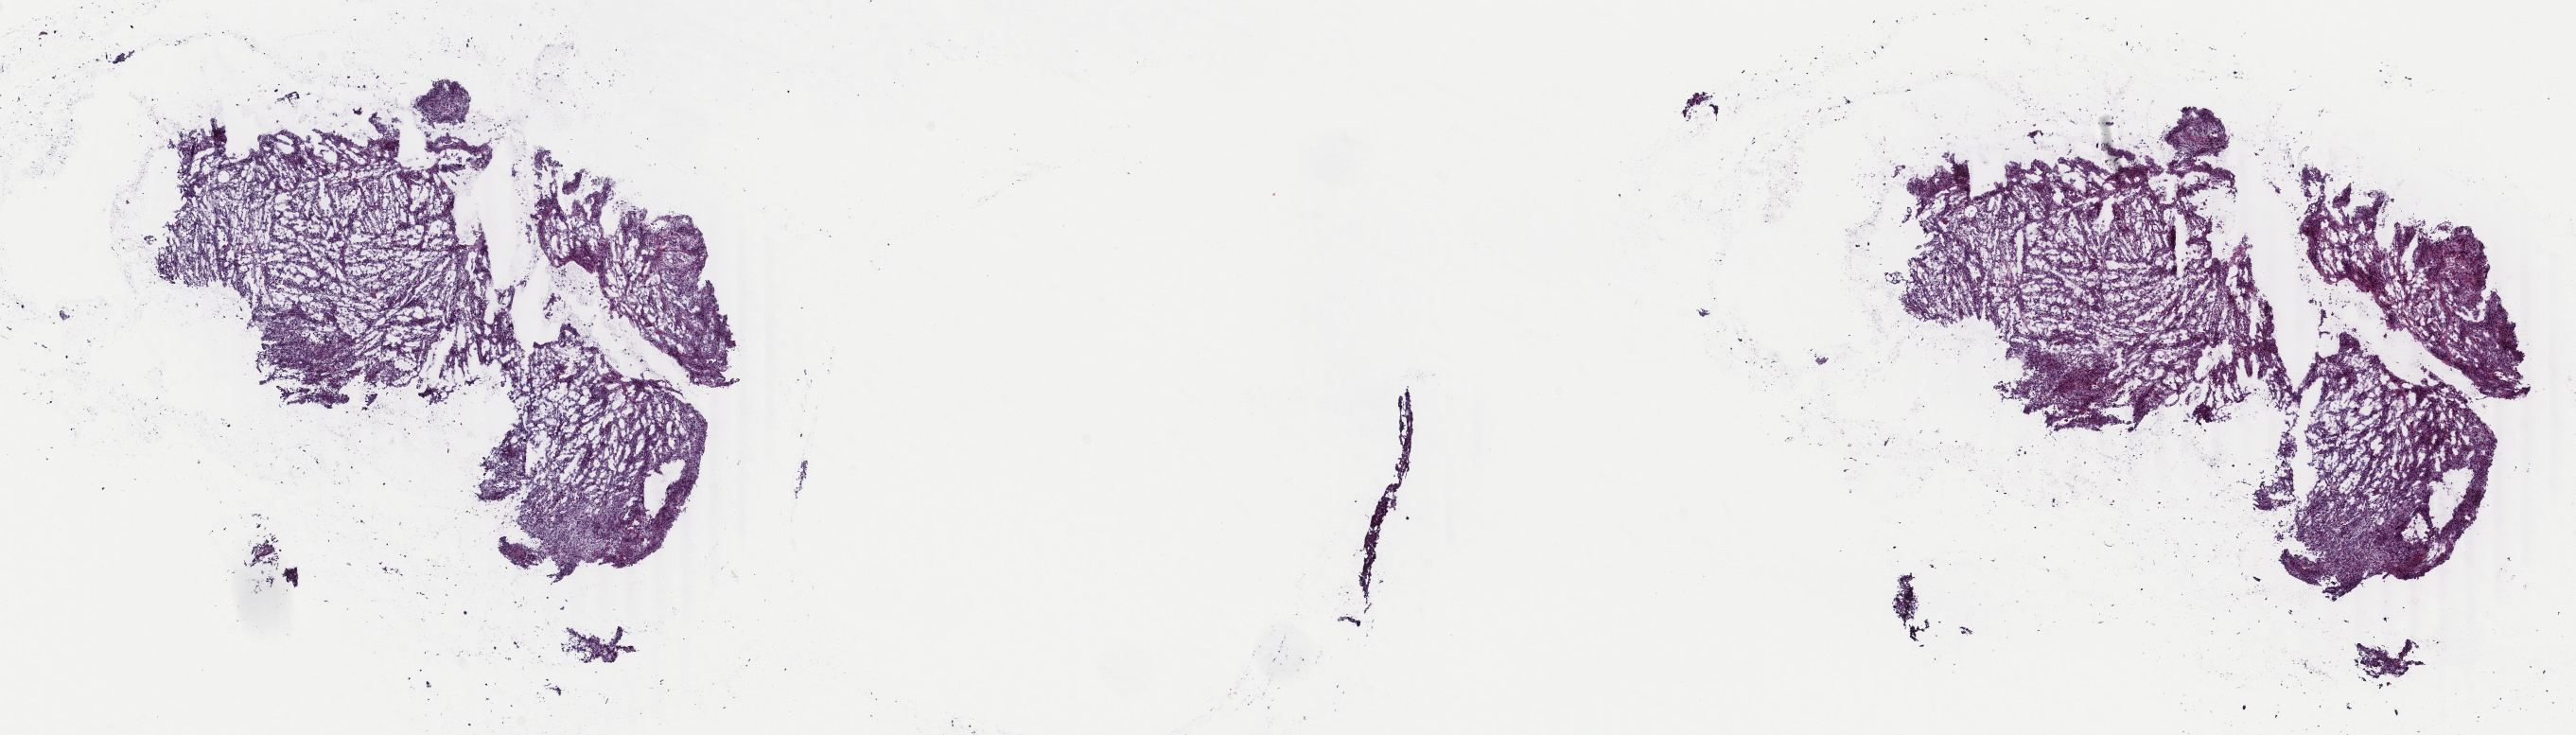
Whole-slide histology image, H&E-stained, whole scanned area (about 21.7 x 6.2 mm) shown as a low-resolution overview; frozen section from the top of the tissue portion; sample: primary tumour, uterus. Patient: female, age at initial diagnosis 61 years. Pathologist review of this section (percent, as recorded): tumour cells 60%, tumour nuclei 60%, normal cells 10%, stromal cells 15%, necrosis 15%. Inflammatory infiltration, as recorded: lymphocyte infiltration 70%, monocyte infiltration 15%, neutrophil infiltration 5%.
Pathologic diagnosis: Mullerian mixed tumor. Lymph nodes positive (case pathology): 0 of 9 examined. FIGO stage: IIIC.